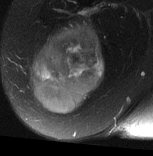
MRI of an extremity soft-tissue mass, one axial slice. Slice 28 of 77 in the series (ordered by position). T2-weighted fat-saturated. MR volume resampled by the dataset authors to the PET/CT grid (not the native acquisition matrix). 153 × 156 image matrix, field of view 149 × 152 mm. Female patient. Case-level facts recorded for this patient, not image findings: histological type: synovial sarcoma; grade: intermediate; site of the primary tumour: right buttock.
Annotated regions visible in this slice (expert contour drawn on MRI and transferred to this co-registered scan by the dataset authors):
- gross tumour volume including surrounding oedema: box from (x=28, y=20) to (x=104, y=114) px
- gross tumour volume (mass): (x=28, y=27)–(x=104, y=114)